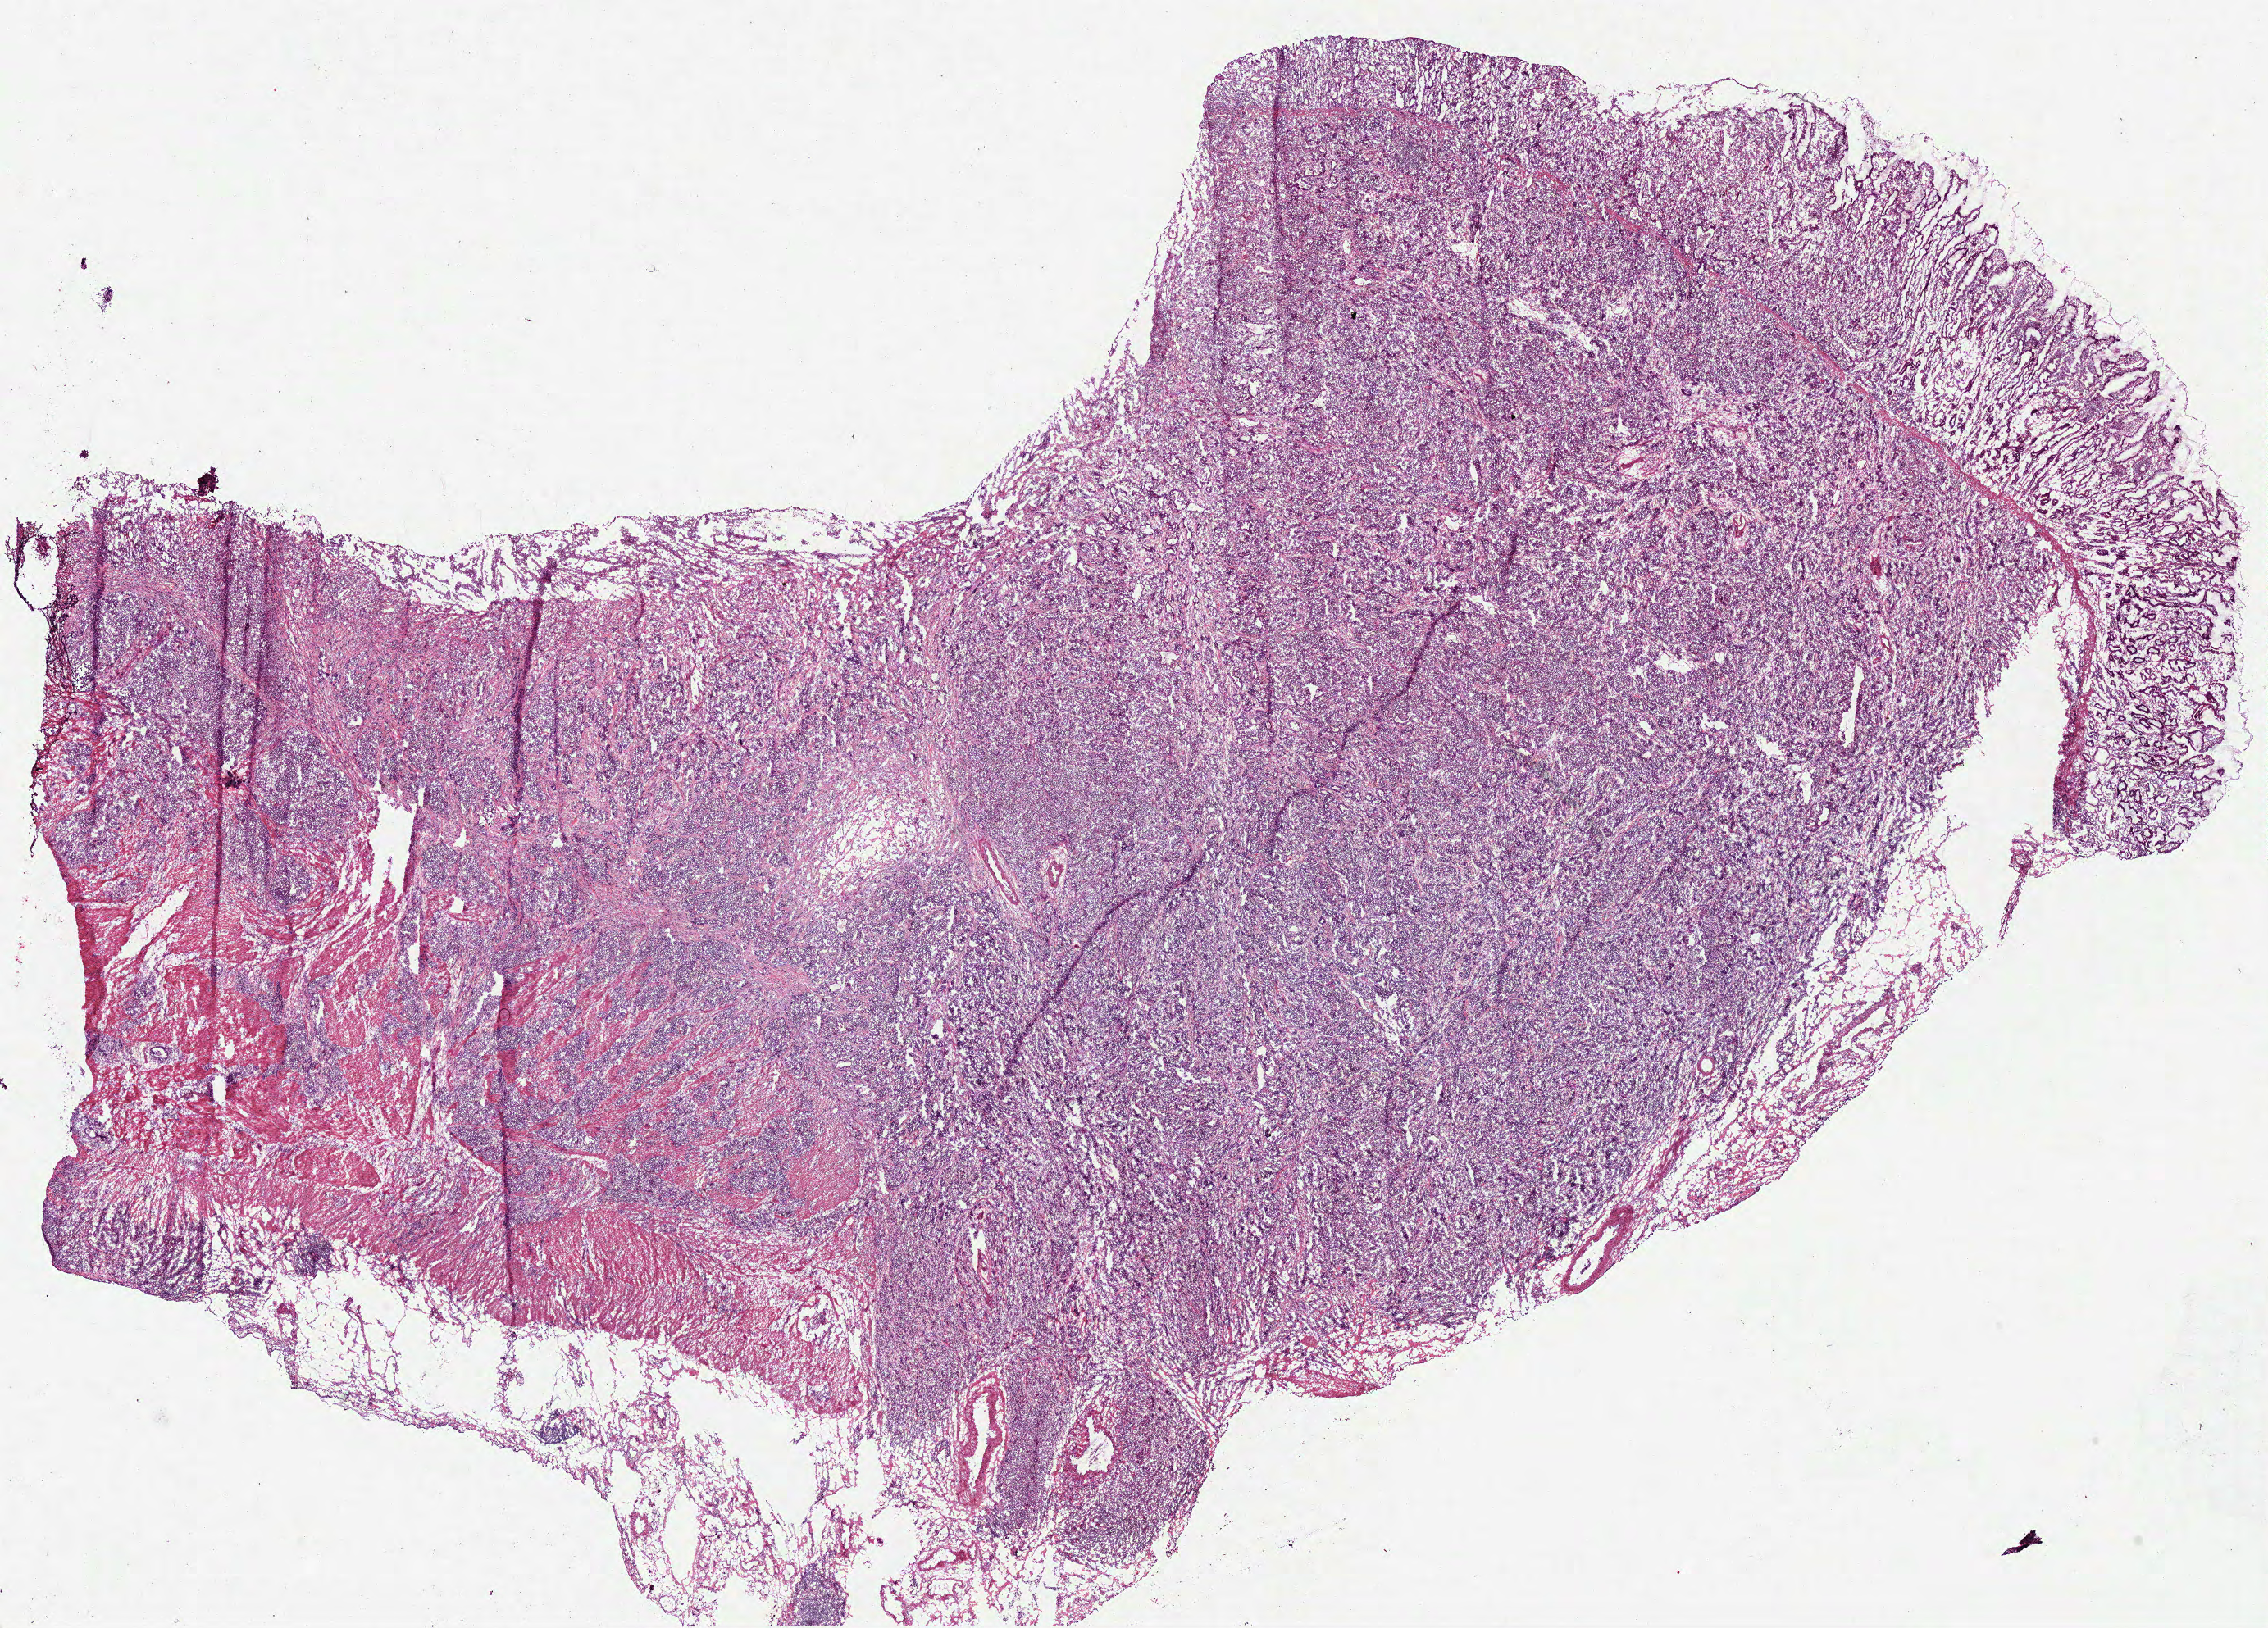
Digitized H&E-stained tissue section (whole slide), shown as a low-resolution overview of the whole scanned area (about 21.8 x 15.7 mm), frozen section from the bottom of the tissue portion, stomach, primary tumour sample. Male, age 59 years at initial diagnosis. Histologic grade: G3 (poorly differentiated). Slide review estimates, as recorded: tumour cells 80%, tumour nuclei 85%, normal cells 10%, stromal cells 10%, necrosis 0%. Infiltration values recorded for this section: lymphocyte infiltration 5%, monocyte infiltration 0%, neutrophil infiltration 2%.
Histologic diagnosis: Adenocarcinoma, NOS (body of stomach). AJCC pathologic stage: IIB.